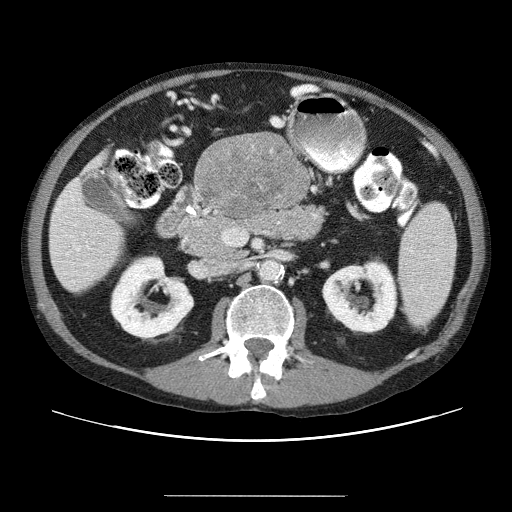
Contrast-enhanced abdominal CT (liver protocol), one axial slice. Slice 9 of 69 in the series (ordered by position). Soft-tissue window (W 400 / L 40 HU). 2.5 mm slice thickness. 512 × 512 image matrix, field of view 380 × 380 mm. From the clinical record (not read from this slice): diagnosis: hepatocellular carcinoma (patient treated with transarterial chemoembolisation; whether this scan precedes or follows treatment is not stated here); TNM stage (as recorded): Stage-IVB; Child-Pugh class: B; tumour differentiation: poorly differentiated; tumour nodularity: multinodular.
Outlined on this slice (semi-automatic segmentation, software-assisted and operator-edited):
- liver parenchyma outside the tumour (the mass and vessels are separate outlines, so this box may not span the whole liver): bounding box (x1, y1, x2, y2) in pixels: (50, 136, 302, 288)
- mass: (190, 136, 311, 225)
- liver vessels: (55, 206, 88, 270)